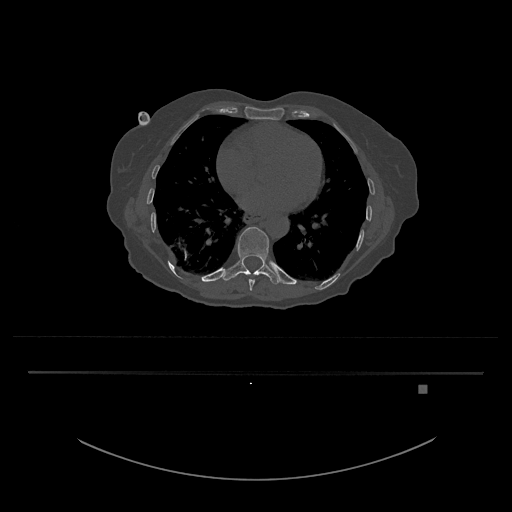
CT including the spine, one axial slice; position 727 of 797 along the scan axis; 120 kVp; bone window (W 1800 / L 400 HU); 0.5 mm slice thickness; 512 × 512 image matrix, field of view 500 × 500 mm. Patient: female, 57 years. From the clinical record (not read from this slice): primary cancer: cervical.
Outlined on this slice (semi-automatically segmented with operator editing):
- T10 vertebra: bounding box (x1, y1, x2, y2) in pixels: (222, 227, 284, 285)
- T9 vertebra: (249, 279, 255, 291)